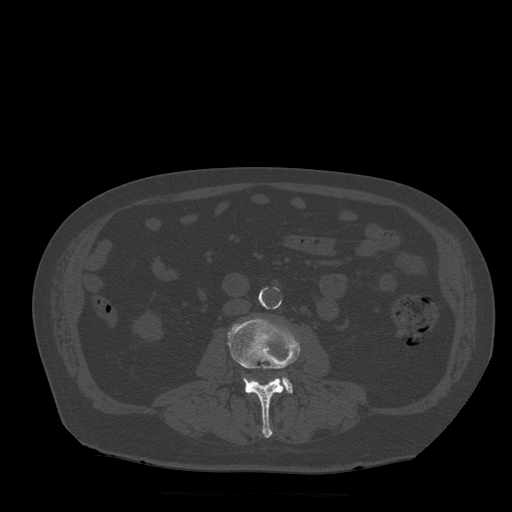
CT including the spine, one axial slice. Position 136 of 522 along the scan axis. Bone window (W 1800 / L 400 HU). 512 × 512 image matrix. Patient age 72 years. Case-level facts recorded for this patient, not image findings: primary cancer: prostate.
Outlined on this slice (semi-automatically segmented with operator editing):
- L3 vertebra: bounding box (x1, y1, x2, y2) in pixels: (228, 318, 300, 438)
- L4 vertebra: (243, 377, 293, 394)